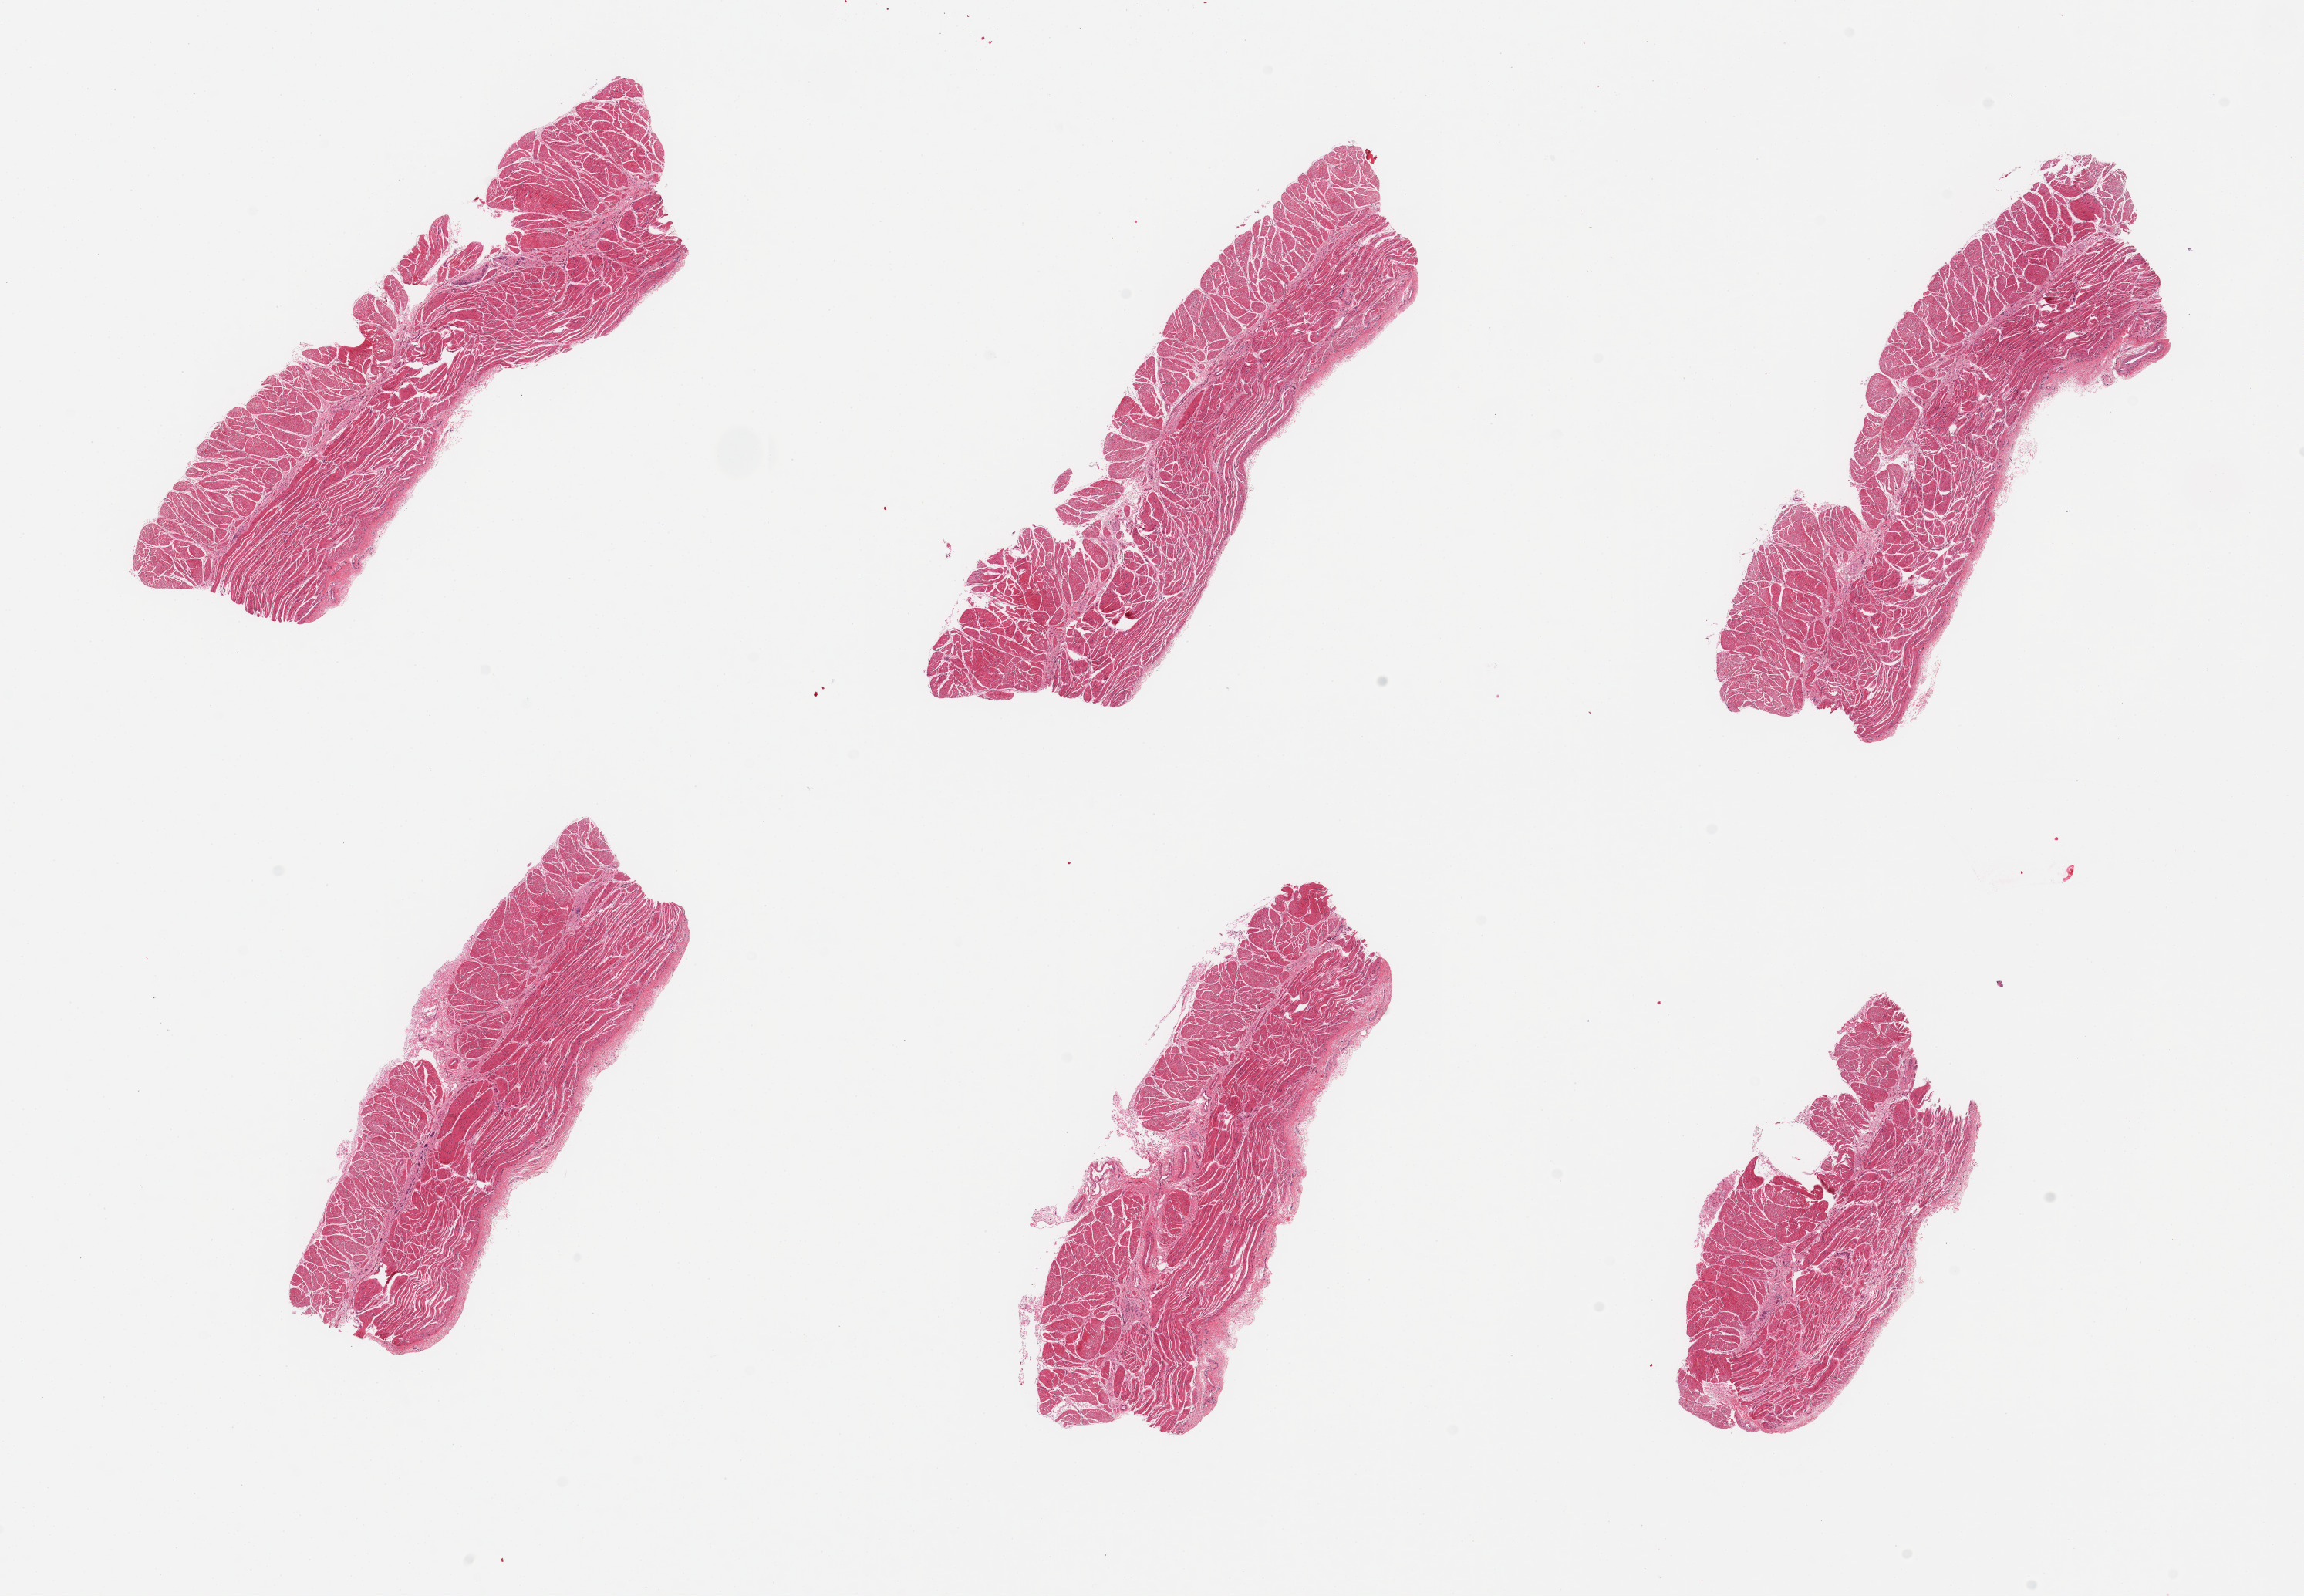
Hematoxylin and eosin (H&E) whole-slide image, shown as a low-resolution overview of the whole scanned area (about 23.6 x 16.4 mm, from a 20x scan). PAXgene-fixed paraffin-embedded (PFPE) section. Sampled site (target tissue): esophageal muscle. Donor tissue sample.
Reviewer comment on this tissue sample: 6 pieces, well trimmed target muscularis.